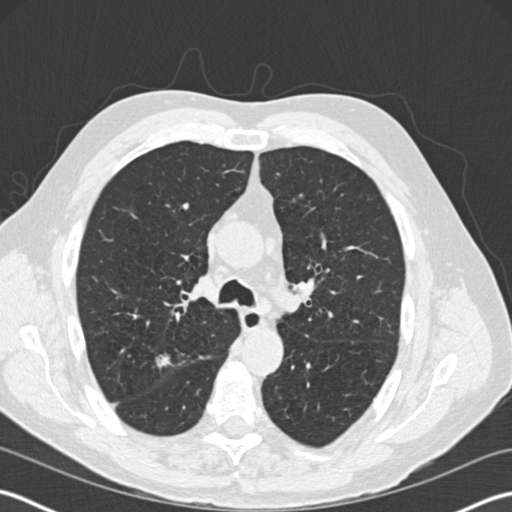
Low-dose screening chest CT, axial slice. Third screening round (two years after baseline). Lung window (W 1500 / L -600 HU). 120 kVp. Slice 74 of 199 in the series. 512 × 512 image matrix. Male participant, aged 65 years at enrolment. Former smoker at enrolment.
Lesion marked by an expert reader, bounding box [x1, y1, x2, y2] px = [142, 345, 181, 379]. The screening reader recorded 6 non-calcified nodules or masses ≥4 mm on this exam (right upper lobe, left upper lobe, left upper lobe, left upper lobe, right upper lobe); which of them this box marks is not recorded. Official screen result: positive, other. Lung cancer was diagnosed 78 days after this screen: adenocarcinoma, NOS, right upper lobe, moderately differentiated (G2), stage IA (AJCC 6th edition), 16 mm at pathology.